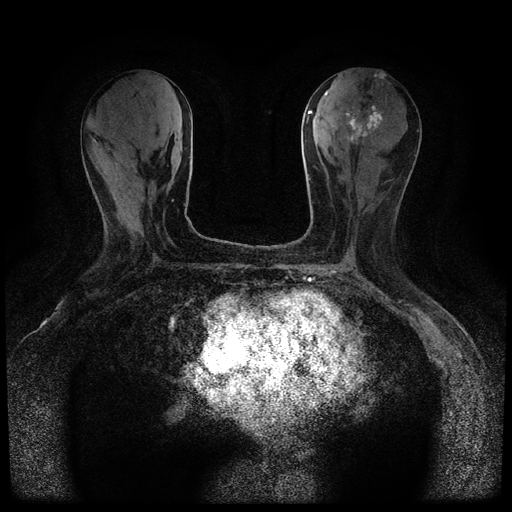
Breast MRI (dynamic contrast-enhanced, multi-phase), one axial slice; position 32 of 116 along the scan axis; dynamic contrast-enhanced series, time point 2 of 5 at this slice position (early post-contrast); 1.5 T; TE 2.7 ms, TR 5.4 ms; 512 × 512 image matrix, field of view 320 × 320 mm. Patient: female, 80 years.
Annotated regions visible in this slice (semi-automatically segmented with operator editing):
- breast lesion (labelled 'tumour' in the annotation; benign lesions carry a separate 'benign' label): bounding box [x1, y1, x2, y2] px = [346, 74, 385, 145]